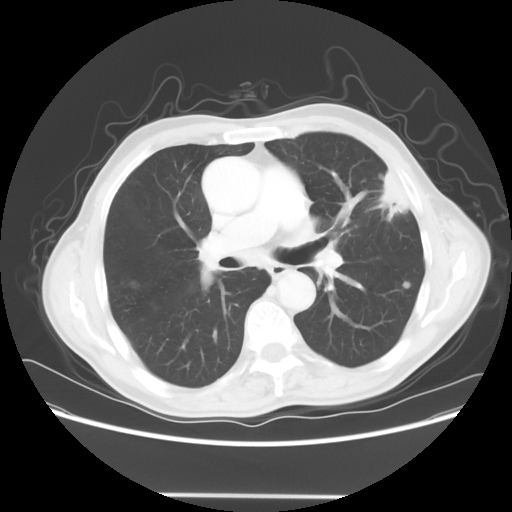
Chest CT, one axial slice; 120 kVp; lung window (W 1500 / L -600 HU); 5 mm slice thickness; 512 × 512 image matrix, field of view 392 × 392 mm. Patient: male, 71 years. From the clinical record (not read from this slice): clinical TNM (as recorded): T1c N0 M0; histopathological grade: G2-3.
Outlined on this slice (bounding box drawn by a radiologist):
- lung tumour (recorded histology: adenocarcinoma): bounding box (x1, y1, x2, y2) in pixels: (374, 164, 413, 229)